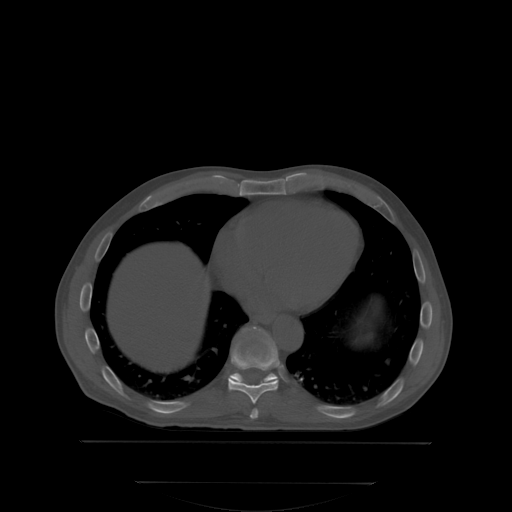
CT including the spine, one axial slice; slice 202 of 350 in the series (ordered by position); bone window (W 1800 / L 400 HU); 2.5 mm slice thickness; 512 × 512 image matrix. Patient: male, 58 years. Case-level facts recorded for this patient, not image findings: primary cancer: prostate.
Structures marked on this image (semi-automatic segmentation, software-assisted and operator-edited):
- T10 vertebra: bounding box (x1, y1, x2, y2) in pixels: (230, 328, 277, 383)
- T8 vertebra: (251, 408, 258, 417)
- T9 vertebra: (228, 331, 279, 403)